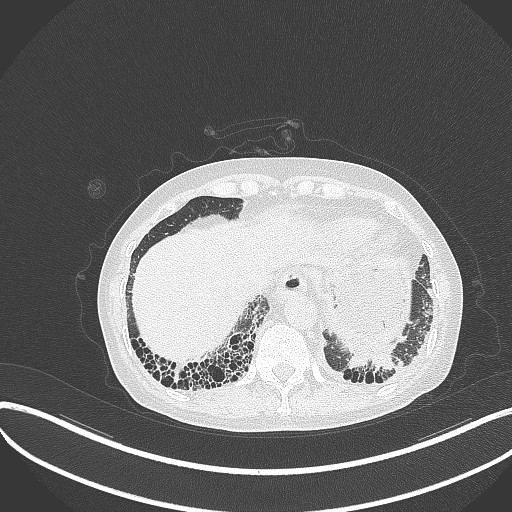
Chest CT, one axial slice. Position 55 of 373 along the scan axis. Reconstruction kernel B70f. Lung window (W 1500 / L -600 HU). 1 mm slice thickness. 512 × 512 image matrix, field of view 400 × 400 mm. Female patient, age 56 years. From the clinical record (not read from this slice): clinical TNM (as recorded): T1 N0 M0.
Outlined on this slice (rectangle marked by the reading radiologist):
- lung tumour (recorded histology: adenocarcinoma): bounding box [x1, y1, x2, y2] px = [343, 346, 400, 378]